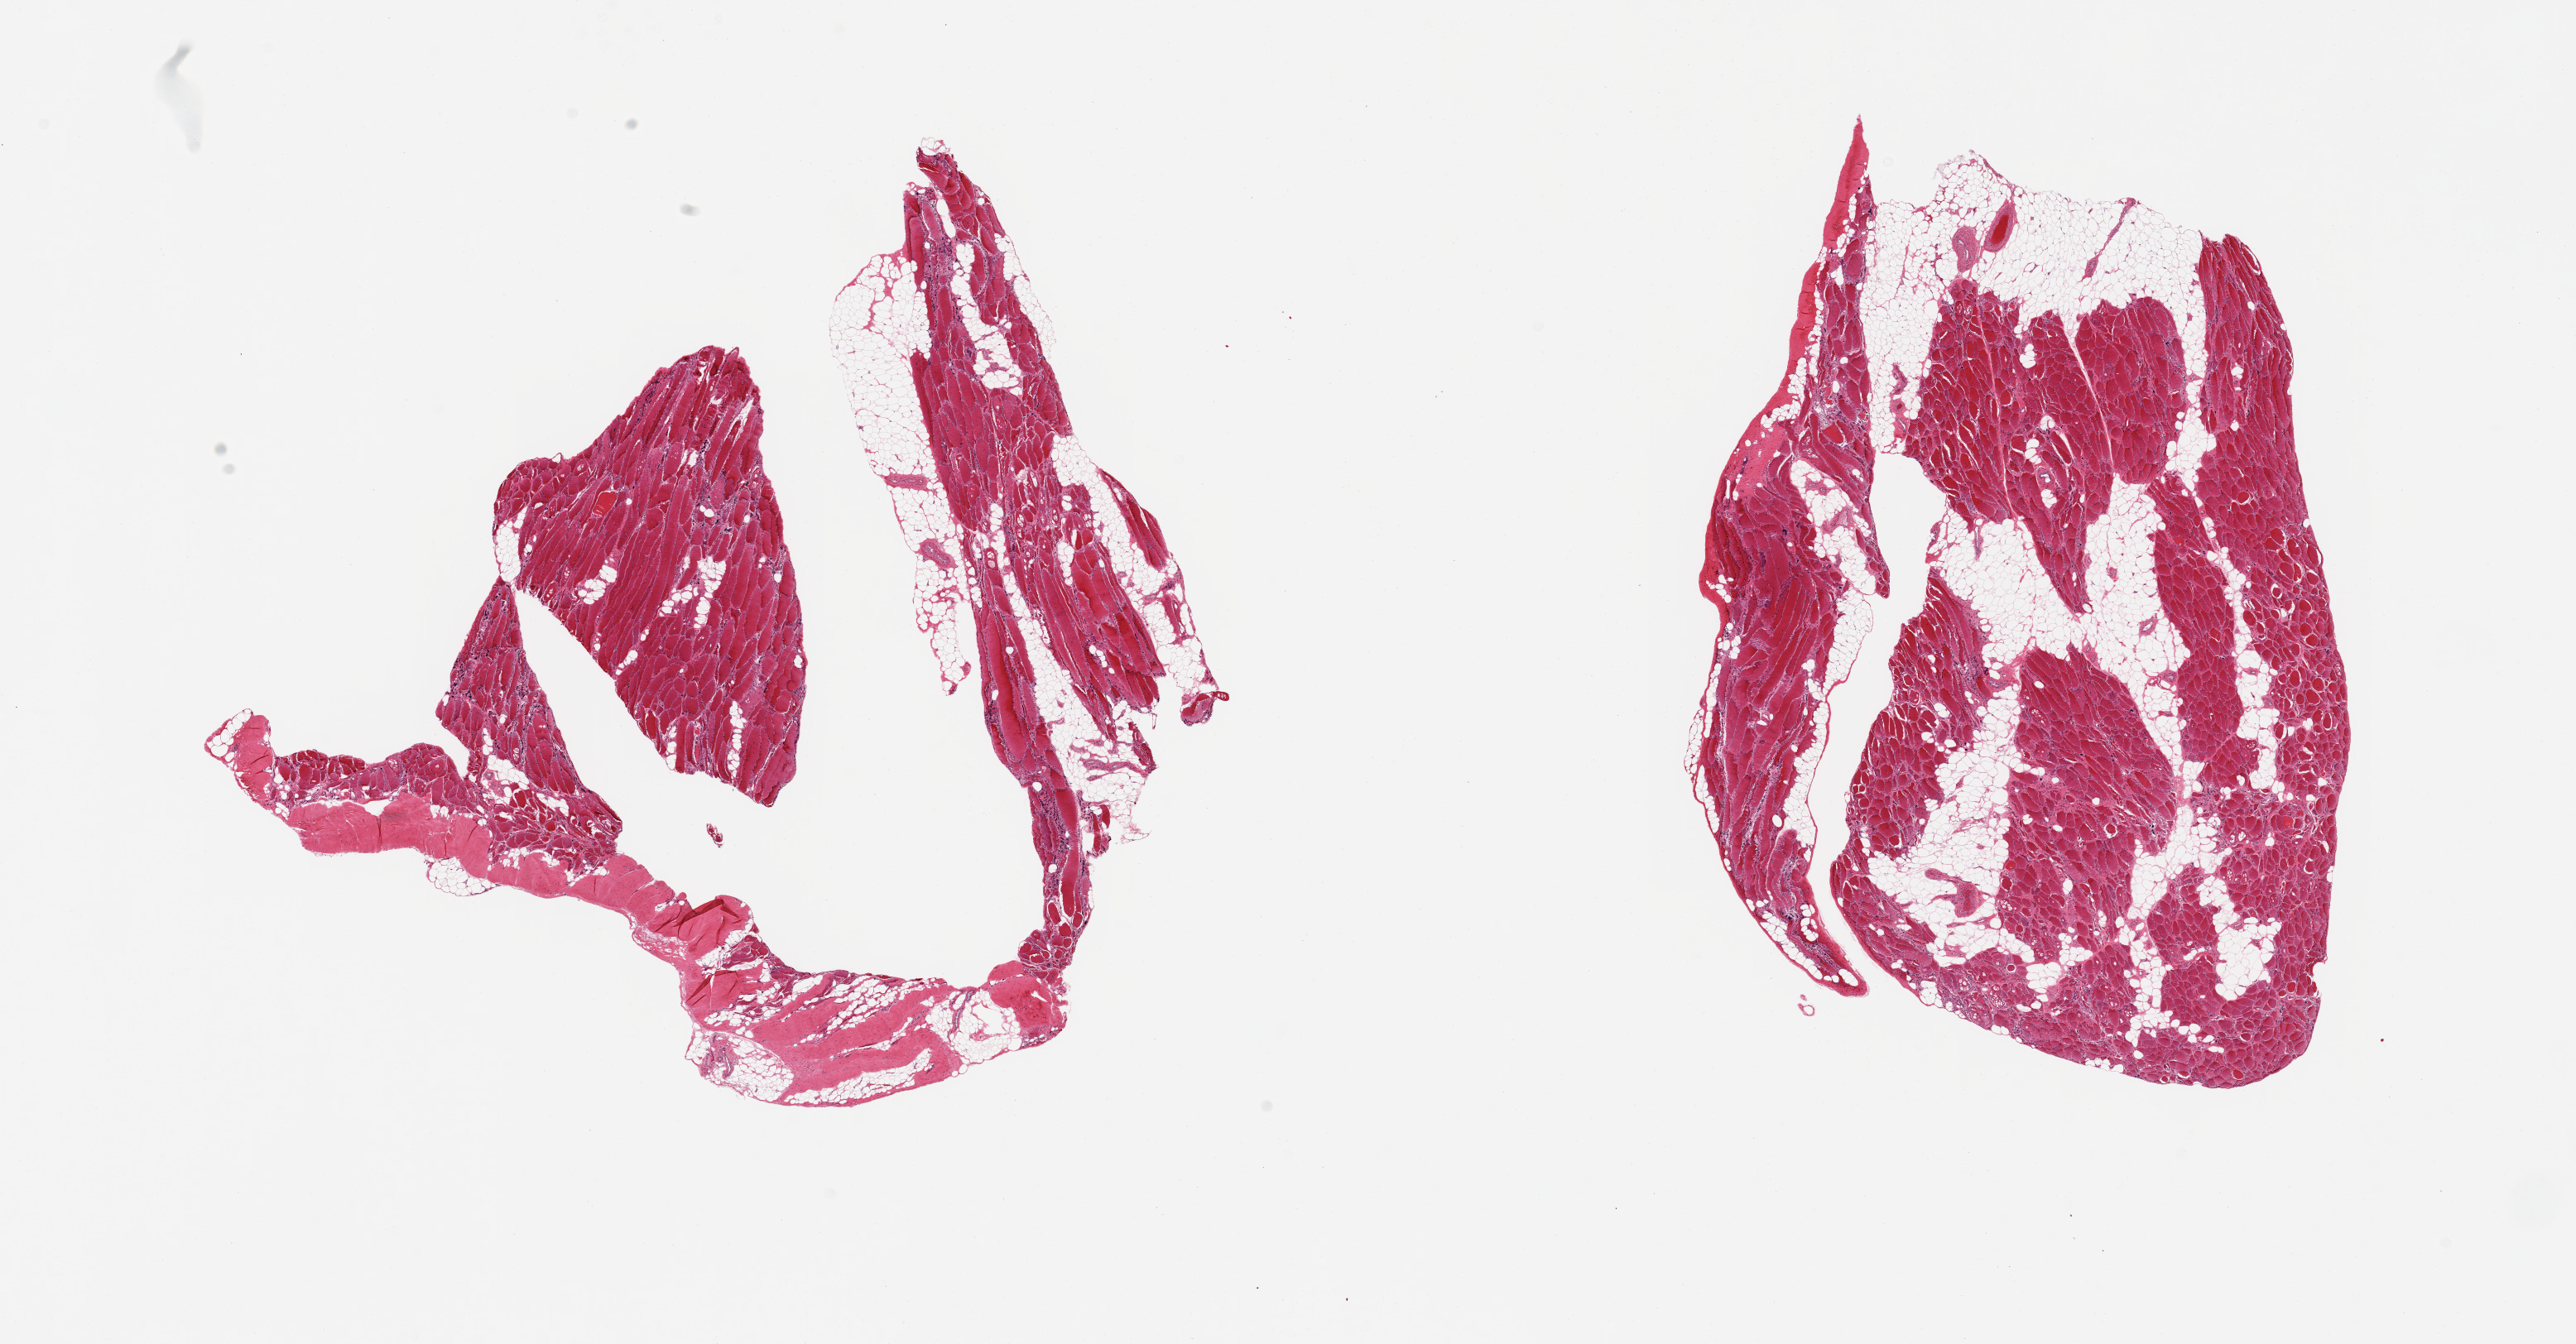
Haematoxylin and eosin whole-slide image, whole scanned area (about 24.6 x 12.8 mm) shown as a low-resolution overview; PAXgene-fixed paraffin-embedded (PFPE) section; target tissue: skeletal muscle; tissue donor sample. Male donor.
* pathologist's review note for this sample: 2 pieces; moderate atrophy with 30% of internal fat